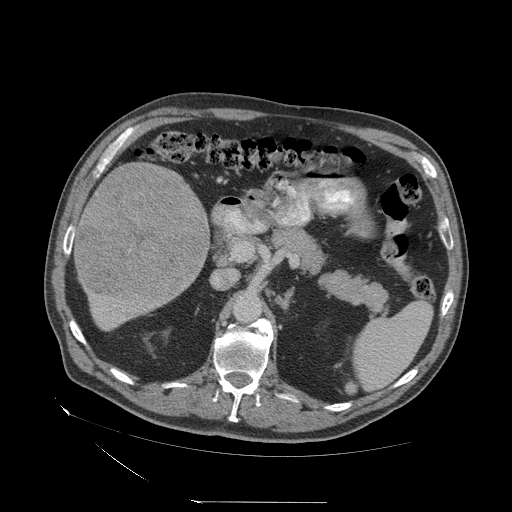
Contrast-enhanced abdominal CT (liver protocol), one axial slice; slice 22 of 83 in the series (ordered by position); 140 kVp; soft-tissue window (W 400 / L 40 HU); 2.5 mm slice thickness; 512 × 512 image matrix, field of view 460 × 460 mm. From the clinical record (not read from this slice): diagnosis: hepatocellular carcinoma (patient treated with transarterial chemoembolisation; whether this scan precedes or follows treatment is not stated here); TNM stage (as recorded): Stage-I; Child-Pugh class: A.
Structures marked on this image (semi-automatic segmentation, software-assisted and operator-edited):
- liver parenchyma outside the tumour (the mass and vessels are separate outlines, so this box may not span the whole liver): bounding box [x1, y1, x2, y2] px = [74, 162, 208, 328]
- mass: [75, 162, 207, 300]